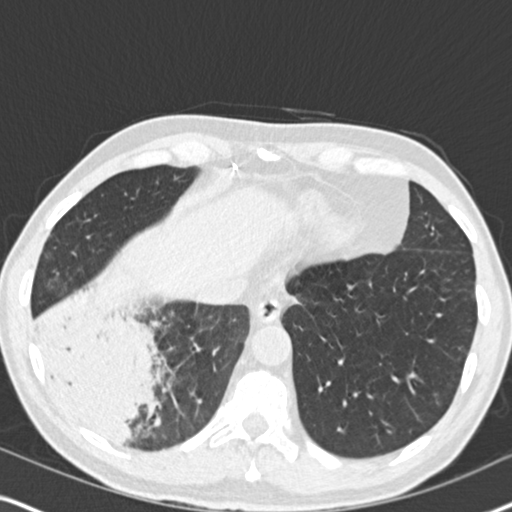
Low-dose screening chest CT, one axial slice. Slice 58 of 182 in the series (ordered by position). Reconstruction kernel B30f. 120 kVp. Lung window (W 1500 / L -600 HU). 512 × 512 image matrix, field of view 330 × 330 mm.
Outlined on this slice (expert manual segmentation):
- lesion 1 (tumor, lower lobe of right lung): bounding box <39,304,153,439> (left, top, right, bottom; pixels)